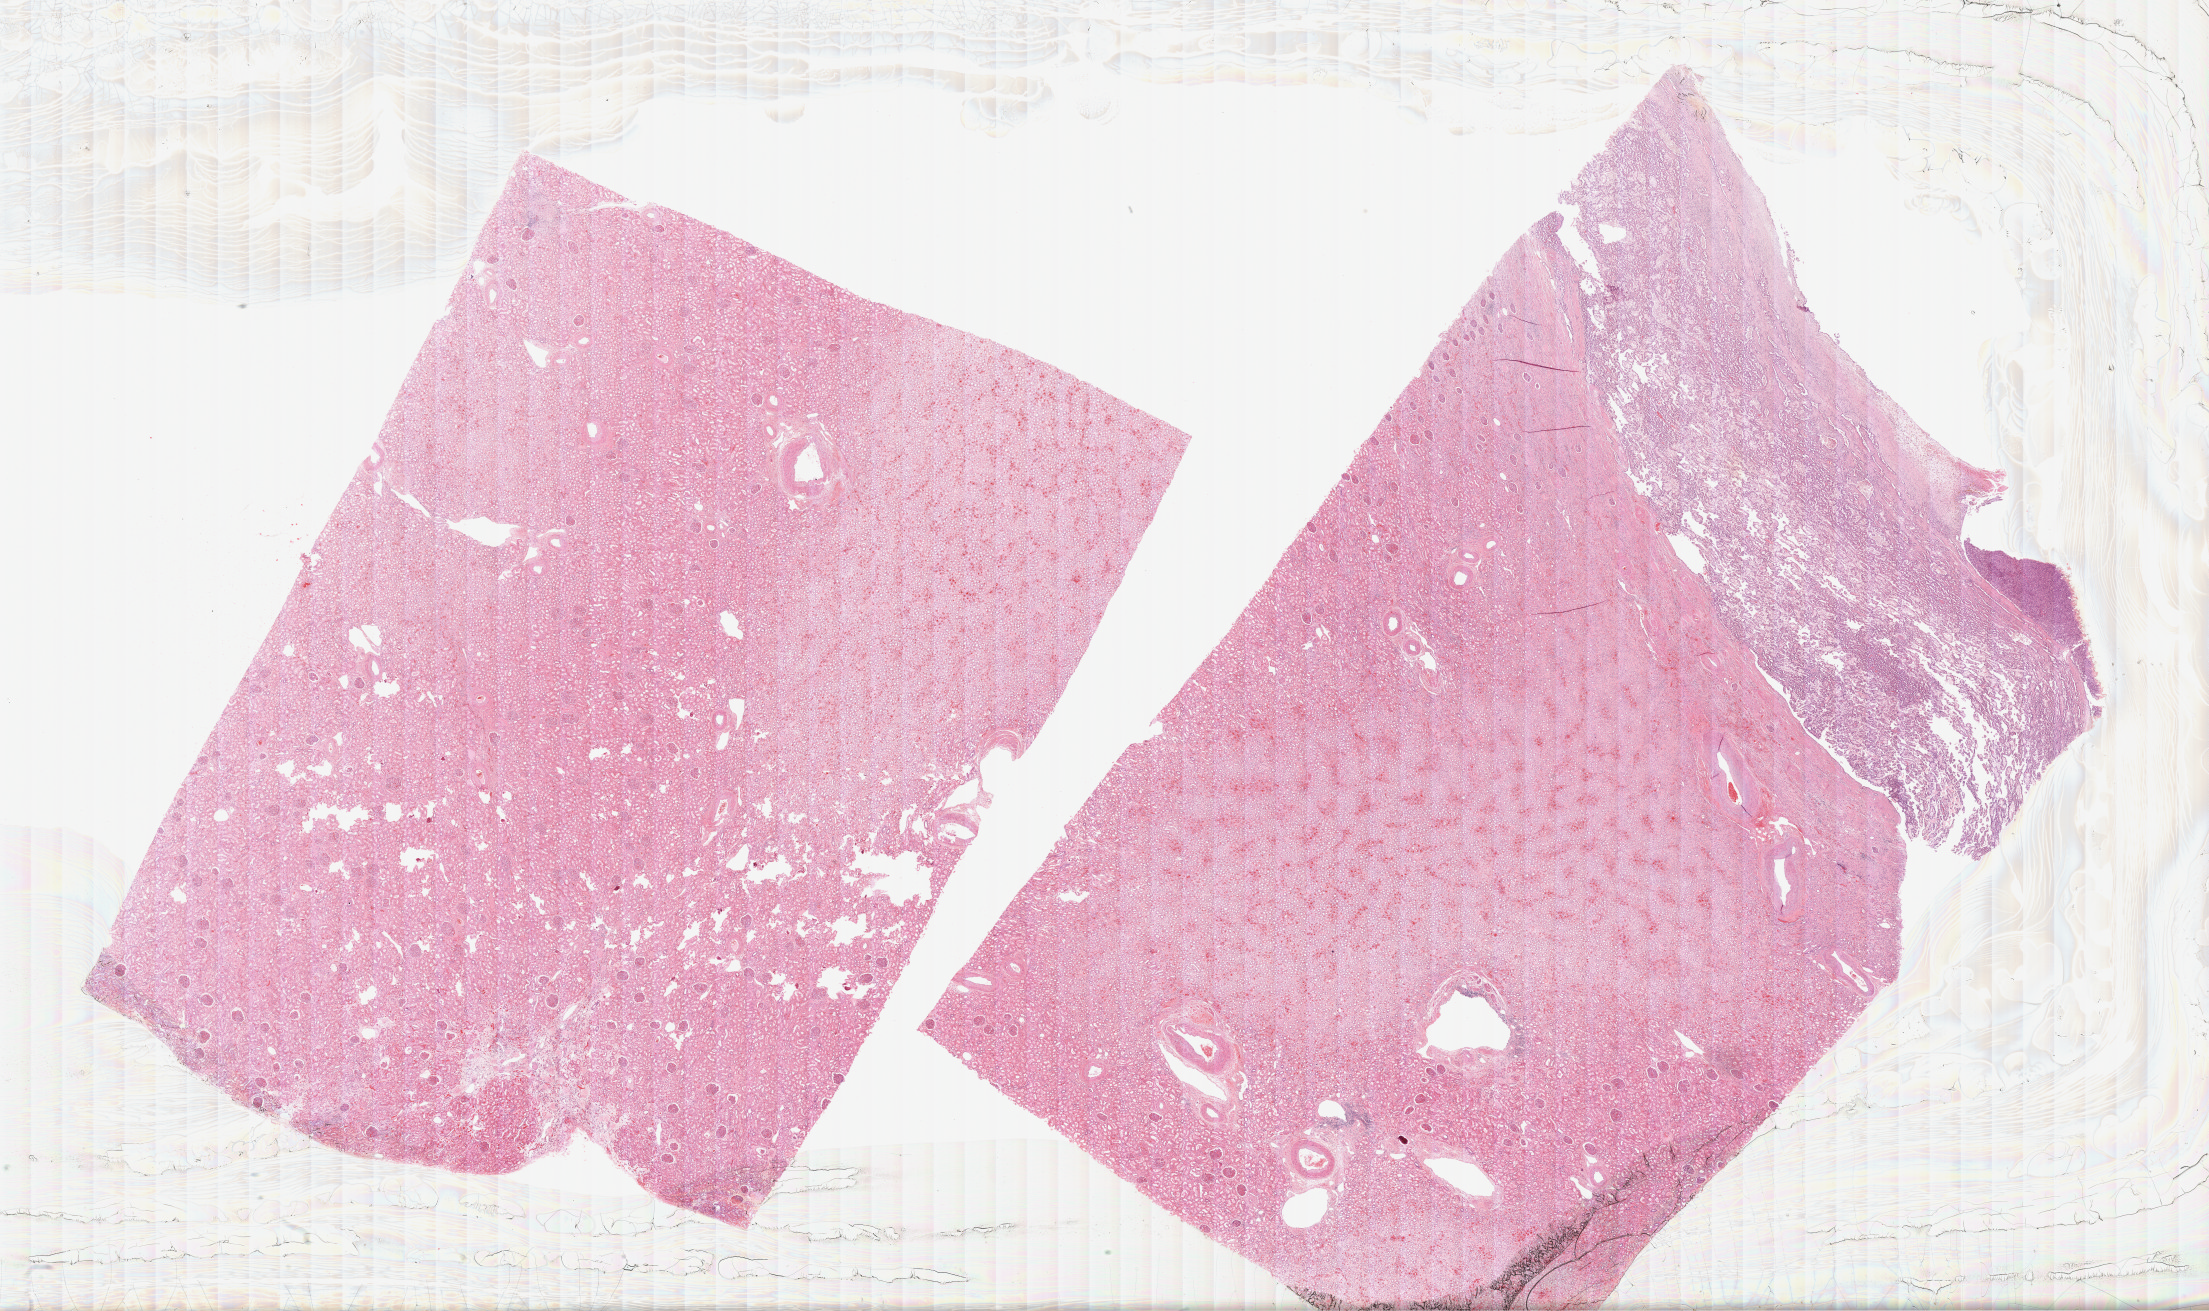
Digitized Hematoxylin and eosin (H&E) stained tissue section (whole slide) — a low-resolution overview of the entire scanned area, about 35.7 x 21.2 mm (slide scanned at 40x); formalin-fixed paraffin-embedded (FFPE) diagnostic section; sample: primary tumour, kidney. Male, age 59 years at initial diagnosis.
Laterality: left. AJCC pathologic stage: II (6th edition). Diagnosis: Papillary adenocarcinoma, NOS.